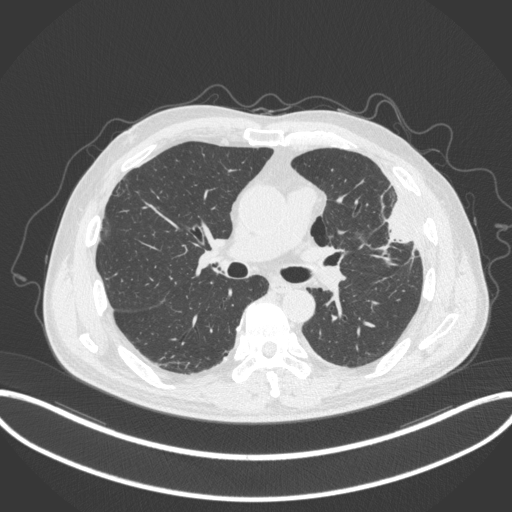
Chest CT, one axial slice; position 194 of 382 along the scan axis; reconstruction kernel B31f; 120 kVp; lung window (W 1500 / L -600 HU); 1 mm slice thickness; 512 × 512 image matrix. Patient: male, 64 years. From the clinical record (not read from this slice): clinical TNM (as recorded): T4 N1 M0; histopathological grade: G3.
Structures marked on this image (rectangle marked by the reading radiologist):
- lung tumour (recorded histology: adenocarcinoma): bounding box [x1, y1, x2, y2] px = [379, 197, 418, 257]